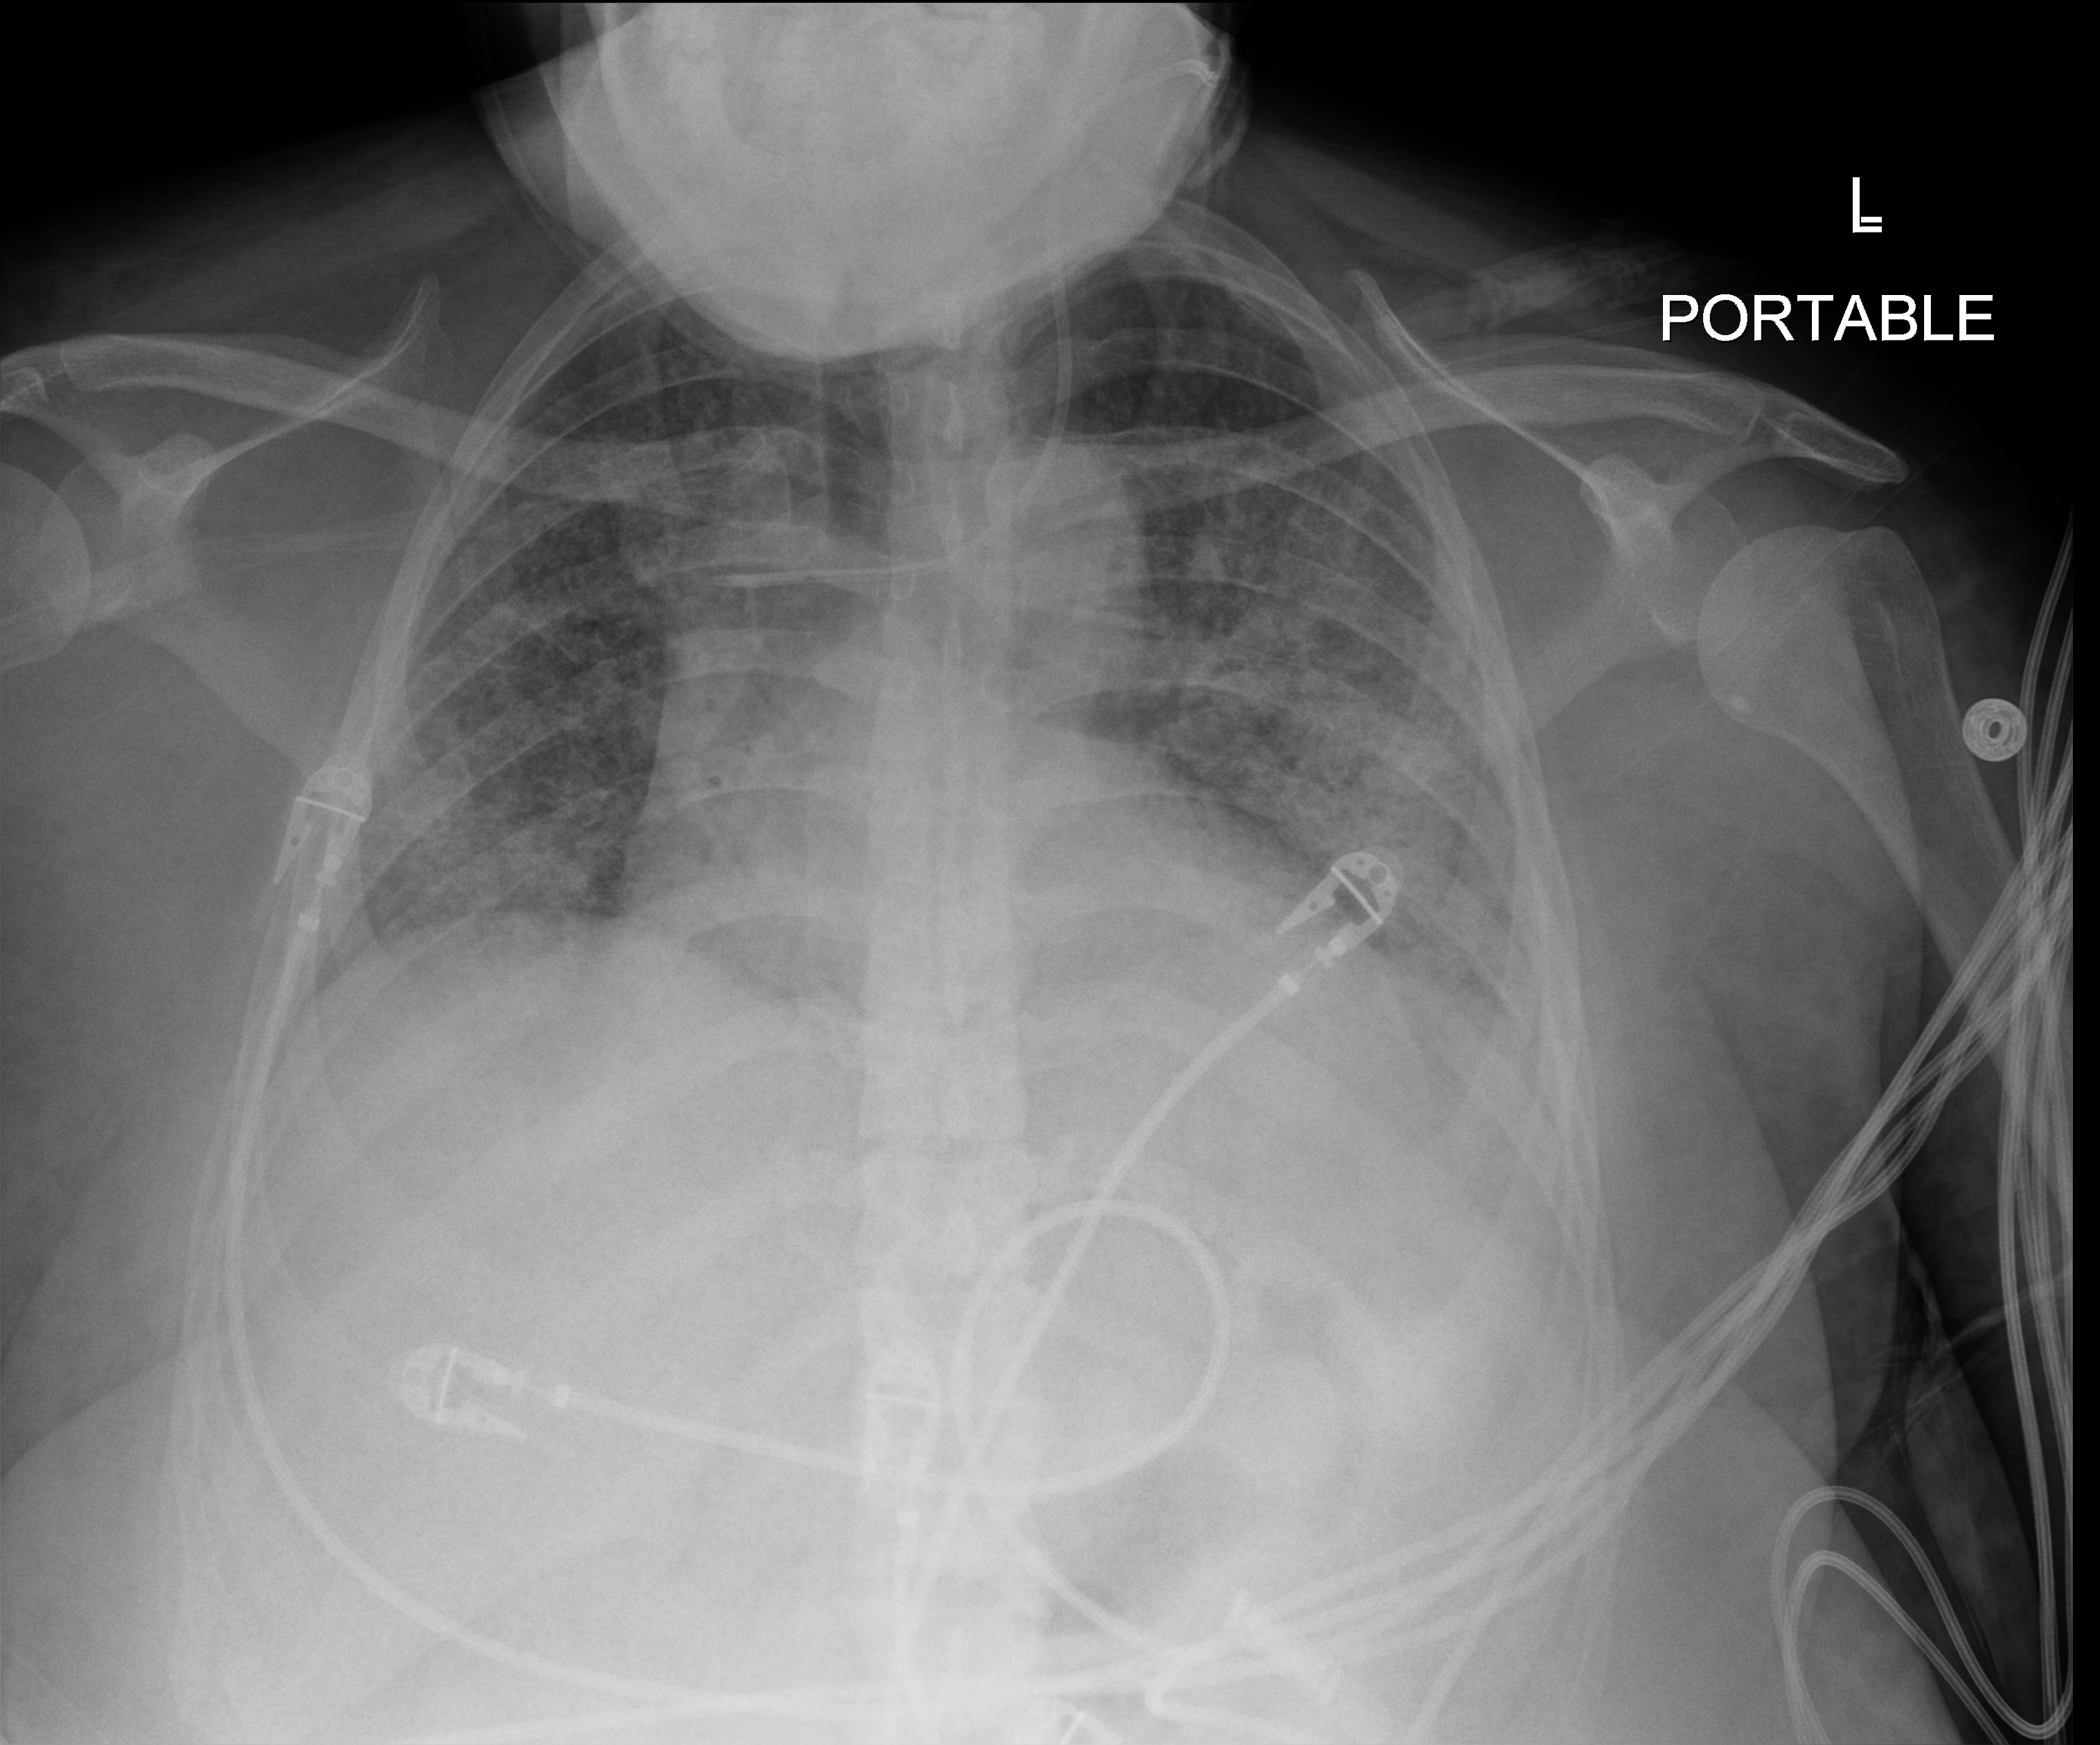
Portable chest radiograph; anteroposterior (AP) projection. Female patient hospitalised with COVID-19, age 18–59 years.
Hospital-stay facts (about this admission, not read from this image; timing relative to this image not recorded):
- admitted to intensive care during this hospital stay: no